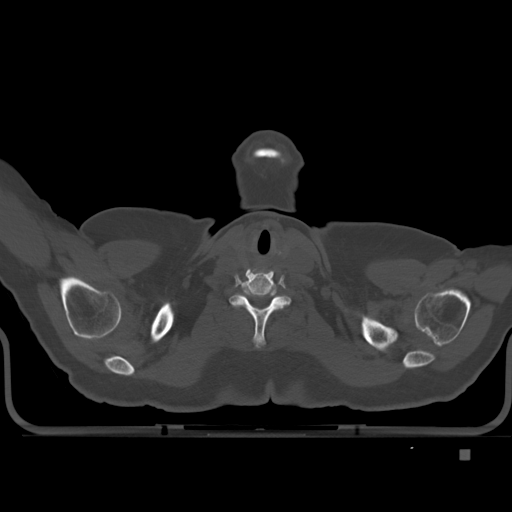
CT including the spine, one axial slice; slice 414 of 477 in the series (ordered by position); bone window (W 1800 / L 400 HU); 1.5 mm slice thickness; 512 × 512 image matrix. Patient: female, 74 years. From the clinical record (not read from this slice): primary cancer: colon.
Structures marked on this image (semi-automatic segmentation, software-assisted and operator-edited):
- T1 vertebra: bounding box <262,311,273,340> (left, top, right, bottom; pixels)